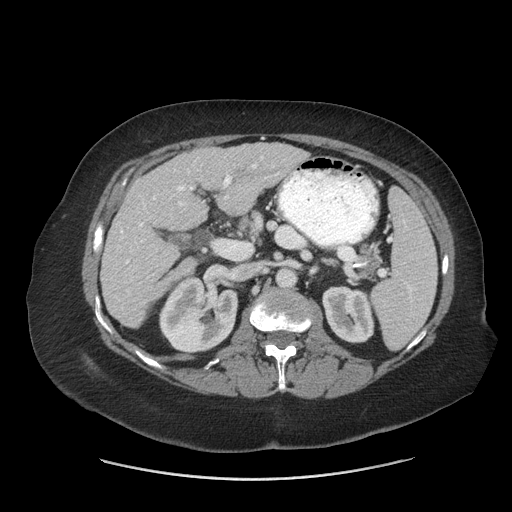
Contrast-enhanced abdominal CT (liver protocol), one axial slice; position 30 of 69 along the scan axis; reconstruction kernel STANDARD; 140 kVp; soft-tissue window (W 400 / L 40 HU); 2.5 mm slice thickness; 512 × 512 image matrix. Case-level facts recorded for this patient, not image findings: diagnosis: hepatocellular carcinoma (patient treated with transarterial chemoembolisation; whether this scan precedes or follows treatment is not stated here); TNM stage (as recorded): Stage-IIIB; Child-Pugh class: A.
Outlined on this slice (semi-automatically segmented with operator editing):
- liver parenchyma outside the tumour (the mass and vessels are separate outlines, so this box may not span the whole liver): bounding box (x1, y1, x2, y2) in pixels: (100, 142, 308, 328)
- liver vessels: (120, 157, 279, 264)